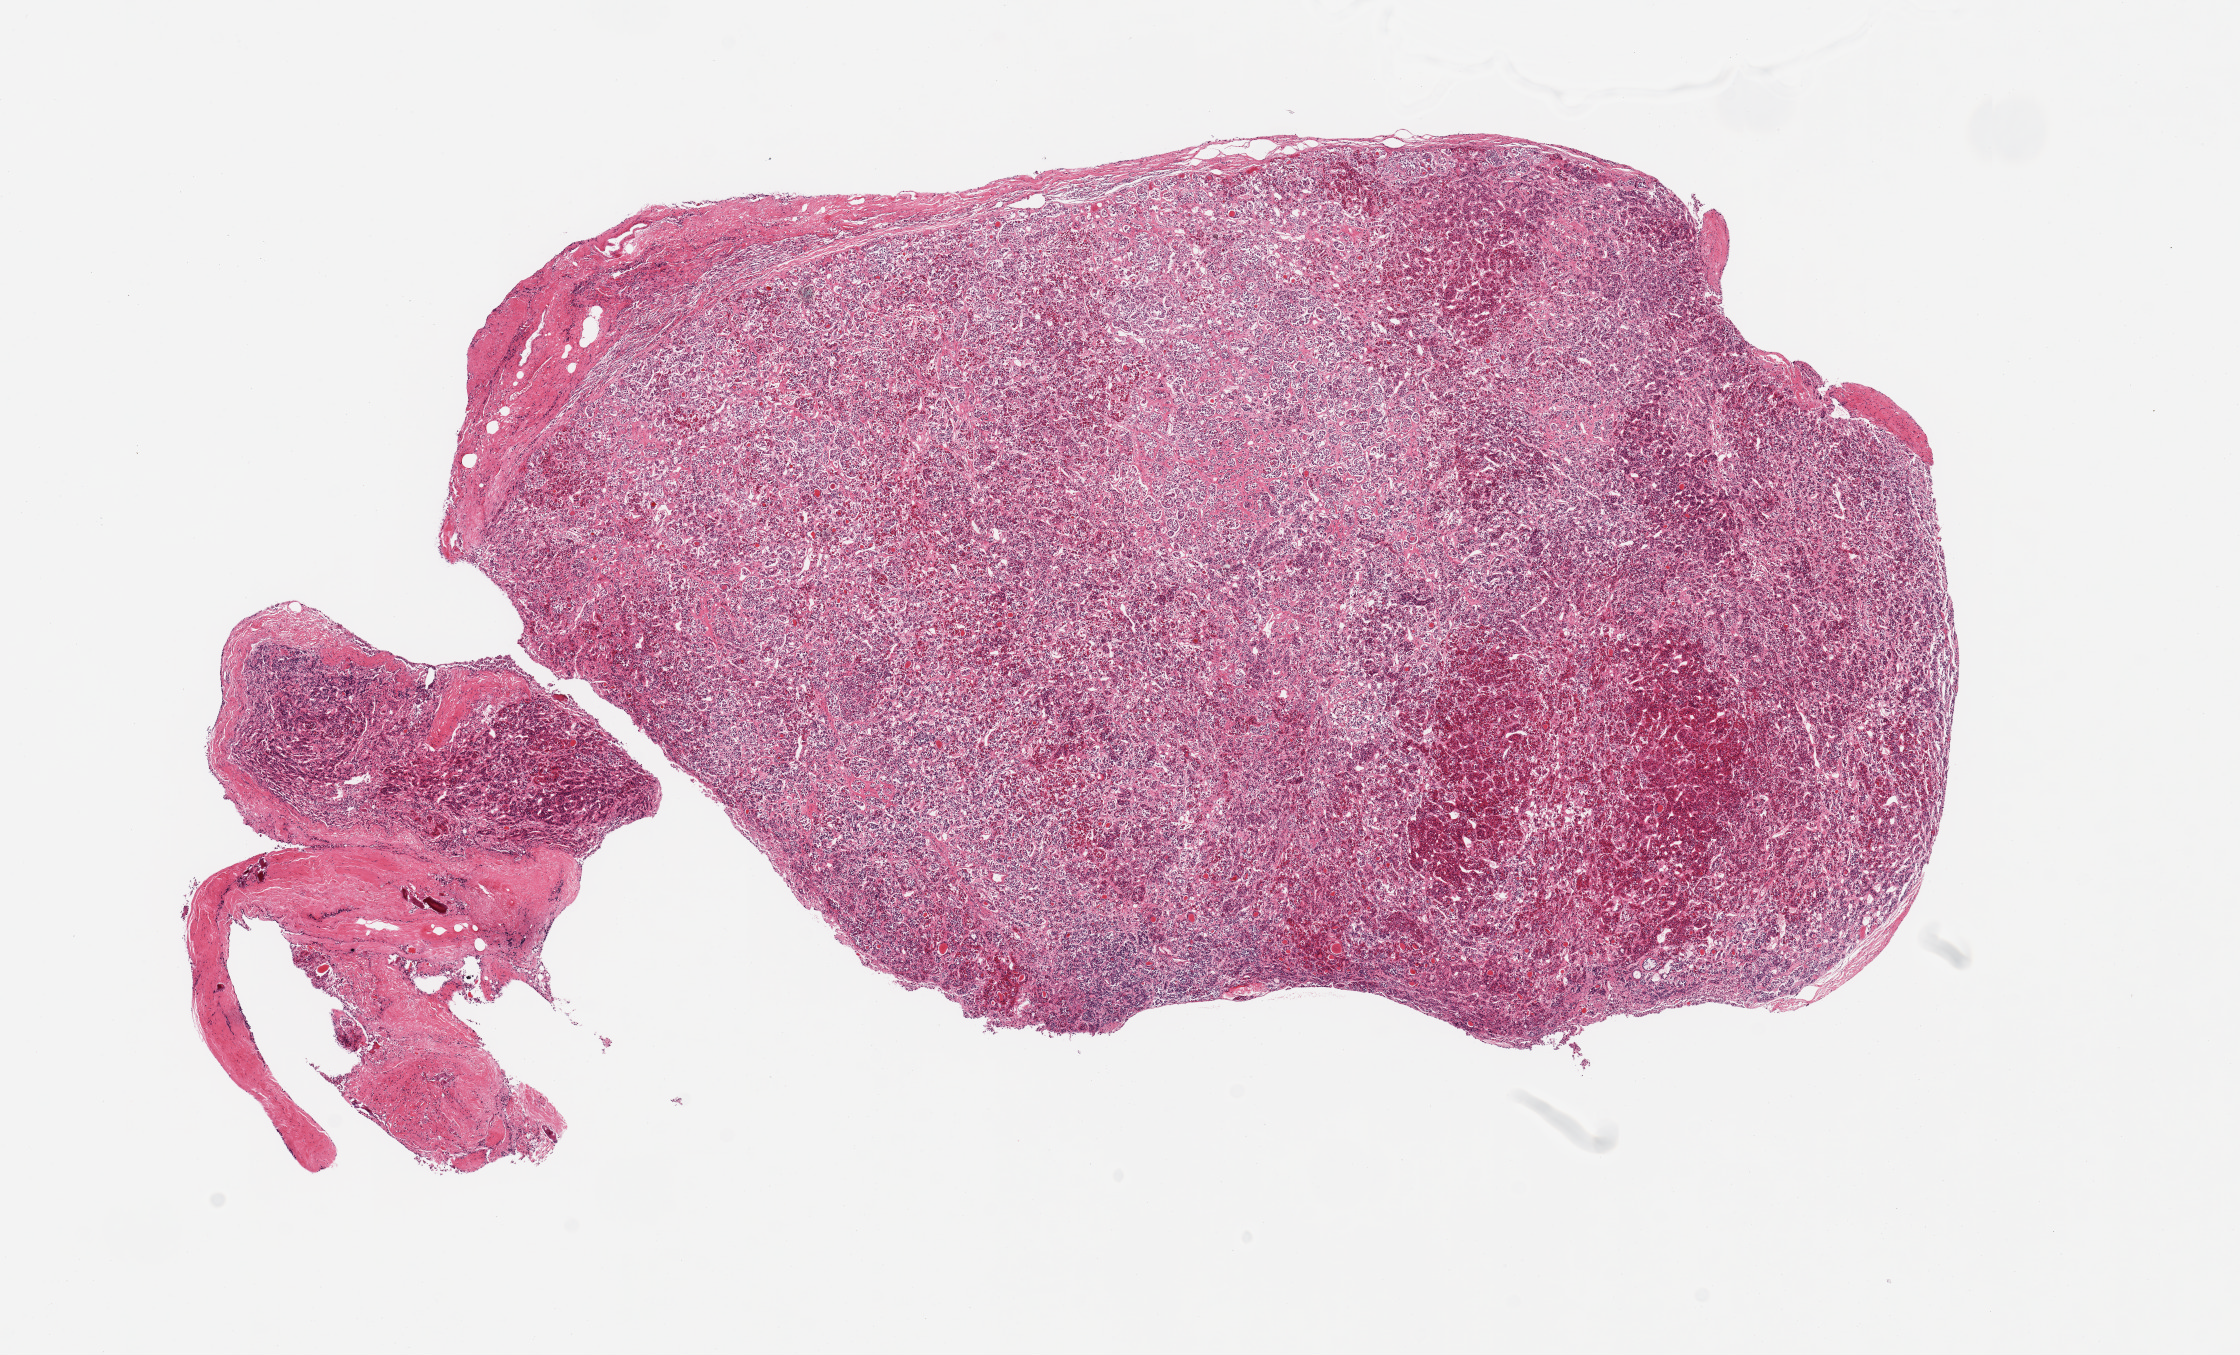
Whole-slide image, H&E stain — whole scanned area (about 17.7 x 10.7 mm, from a 20x scan) shown as a low-resolution overview, PAXgene-fixed paraffin-embedded (PFPE) section, sampled site (target tissue): pituitary, tissue donor sample. Female donor.
* review note (as recorded): 2 pieces (fragmented); adenohypophysis and portion of dura